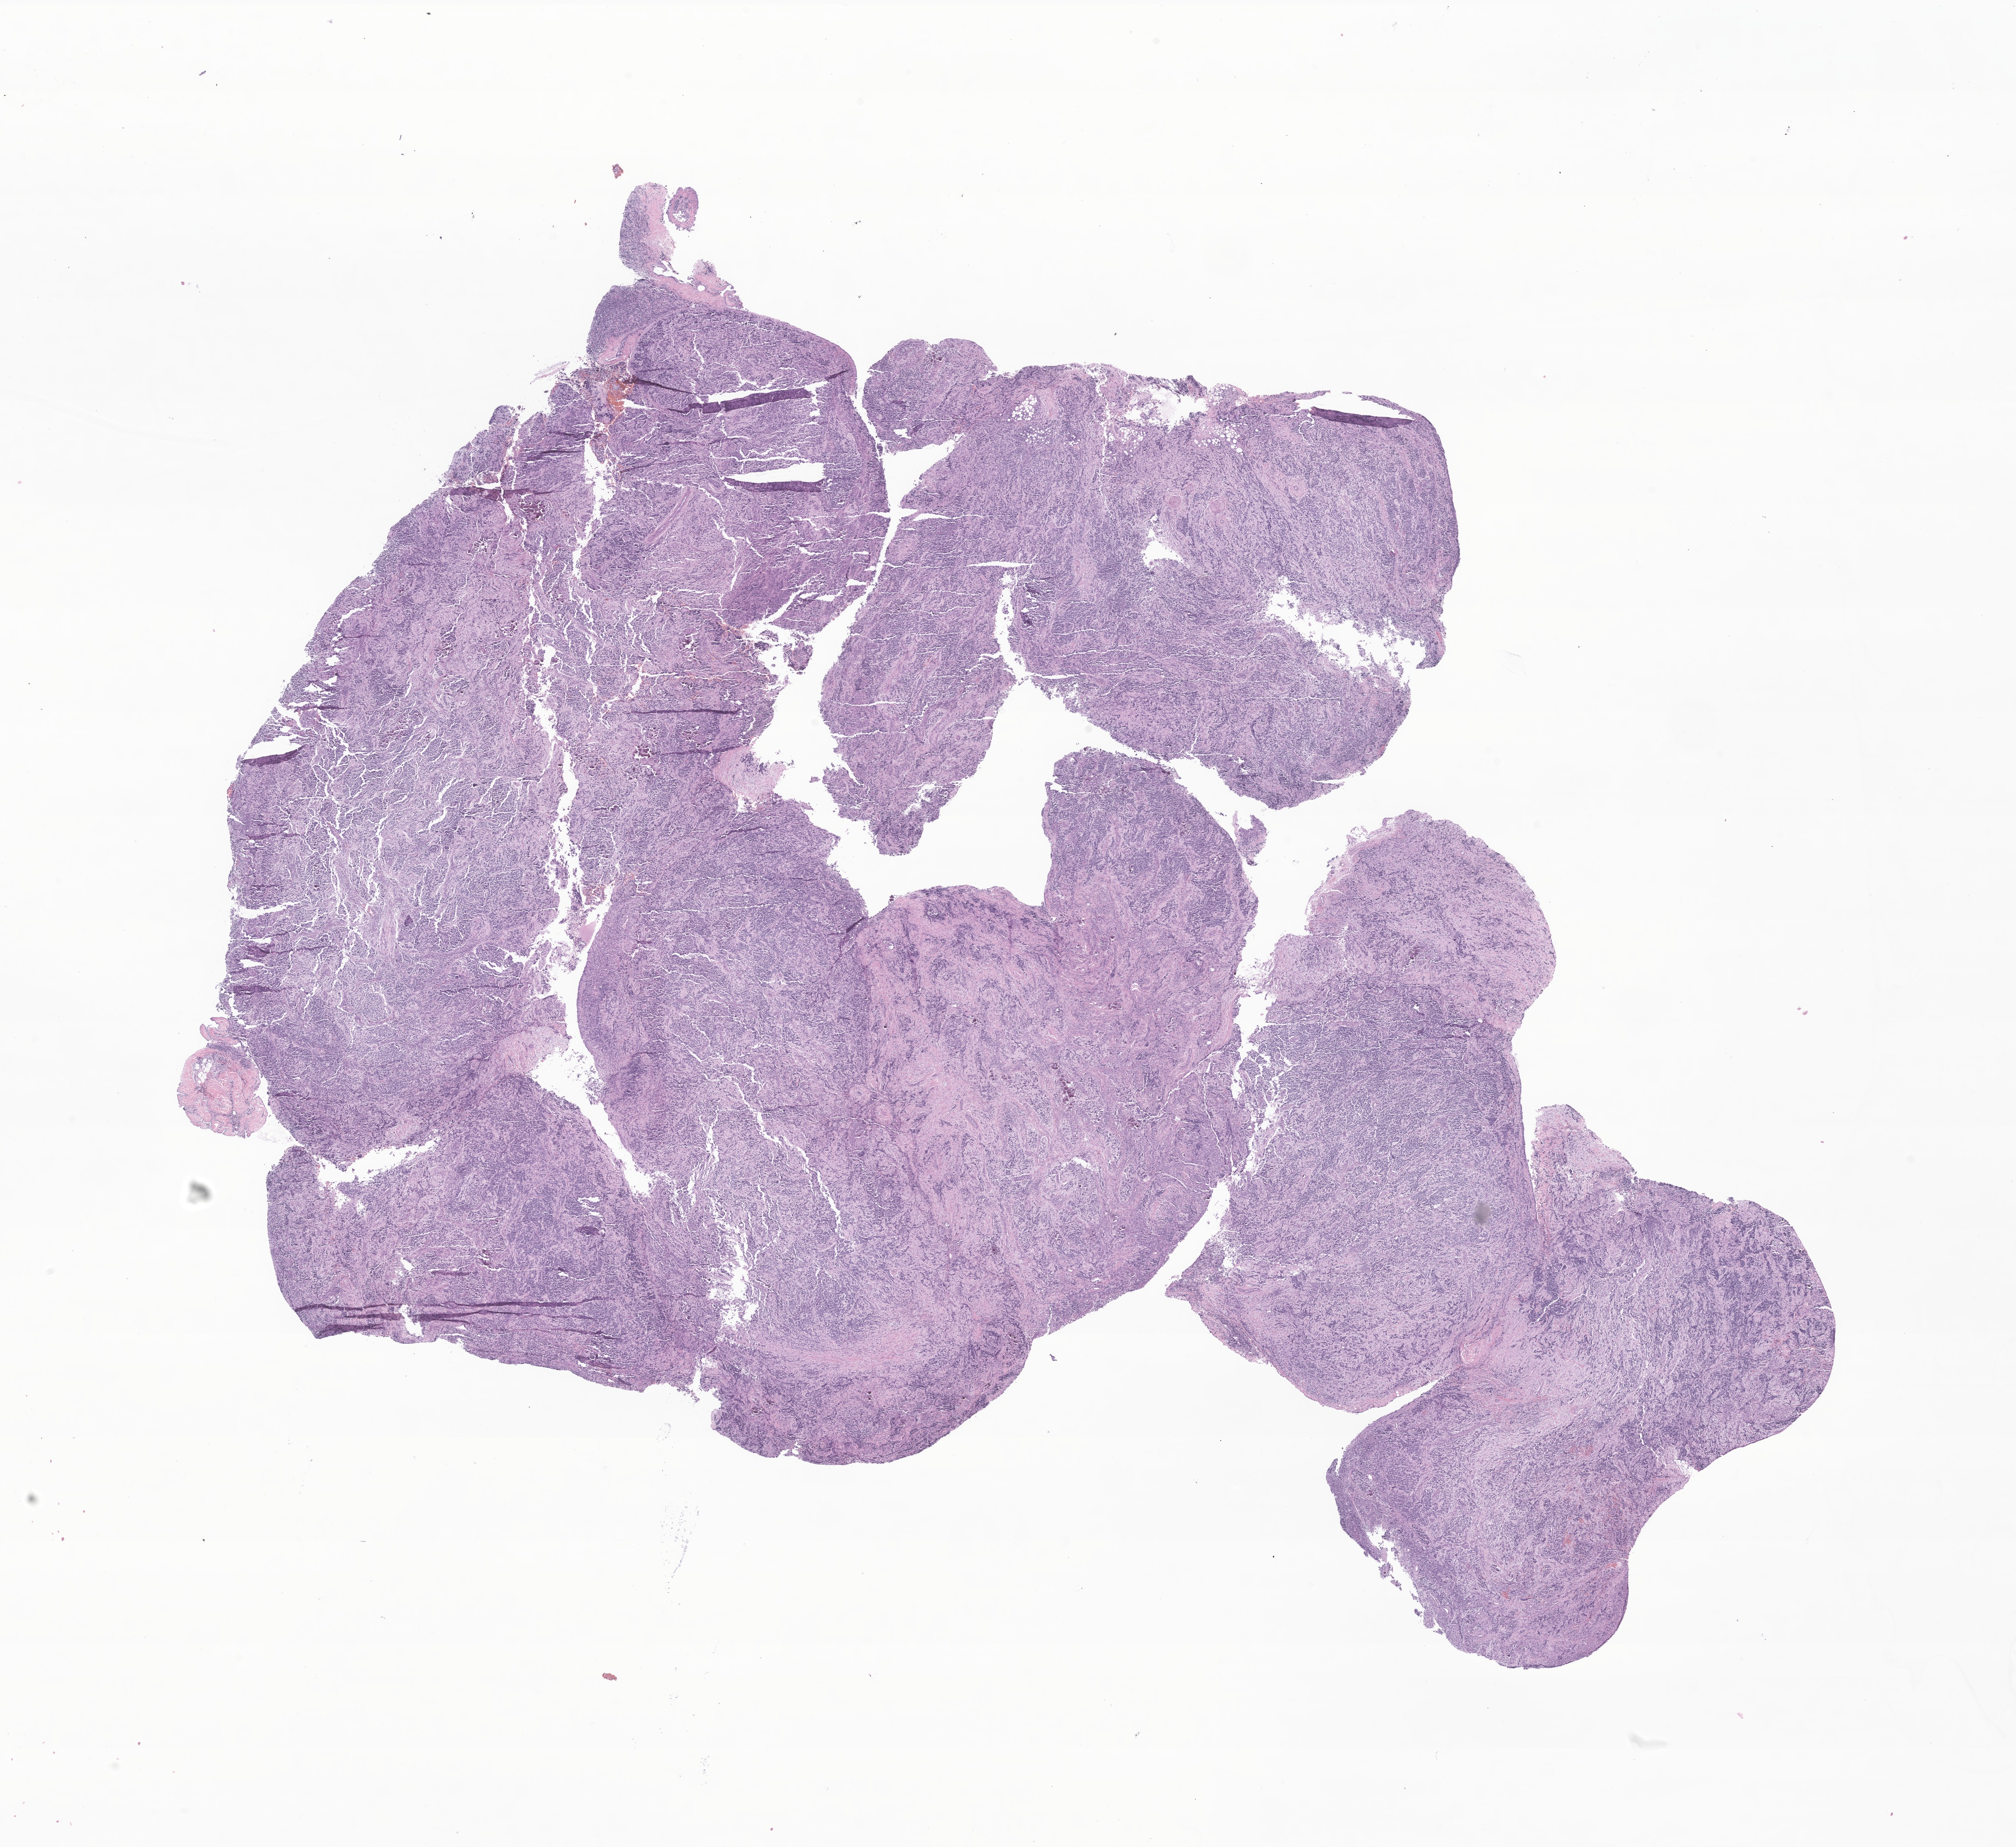
Digitized H&E-stained section of tumor tissue from the soft tissue of thorax — whole scanned area (about 20.8 x 19.0 mm) shown as a low-resolution overview. Formalin-fixed, paraffin-embedded (FFPE) tissue. Patient female; age 535 days.
* diagnosis (ICD-O-3 morphology term): Neuroblastoma, NOS